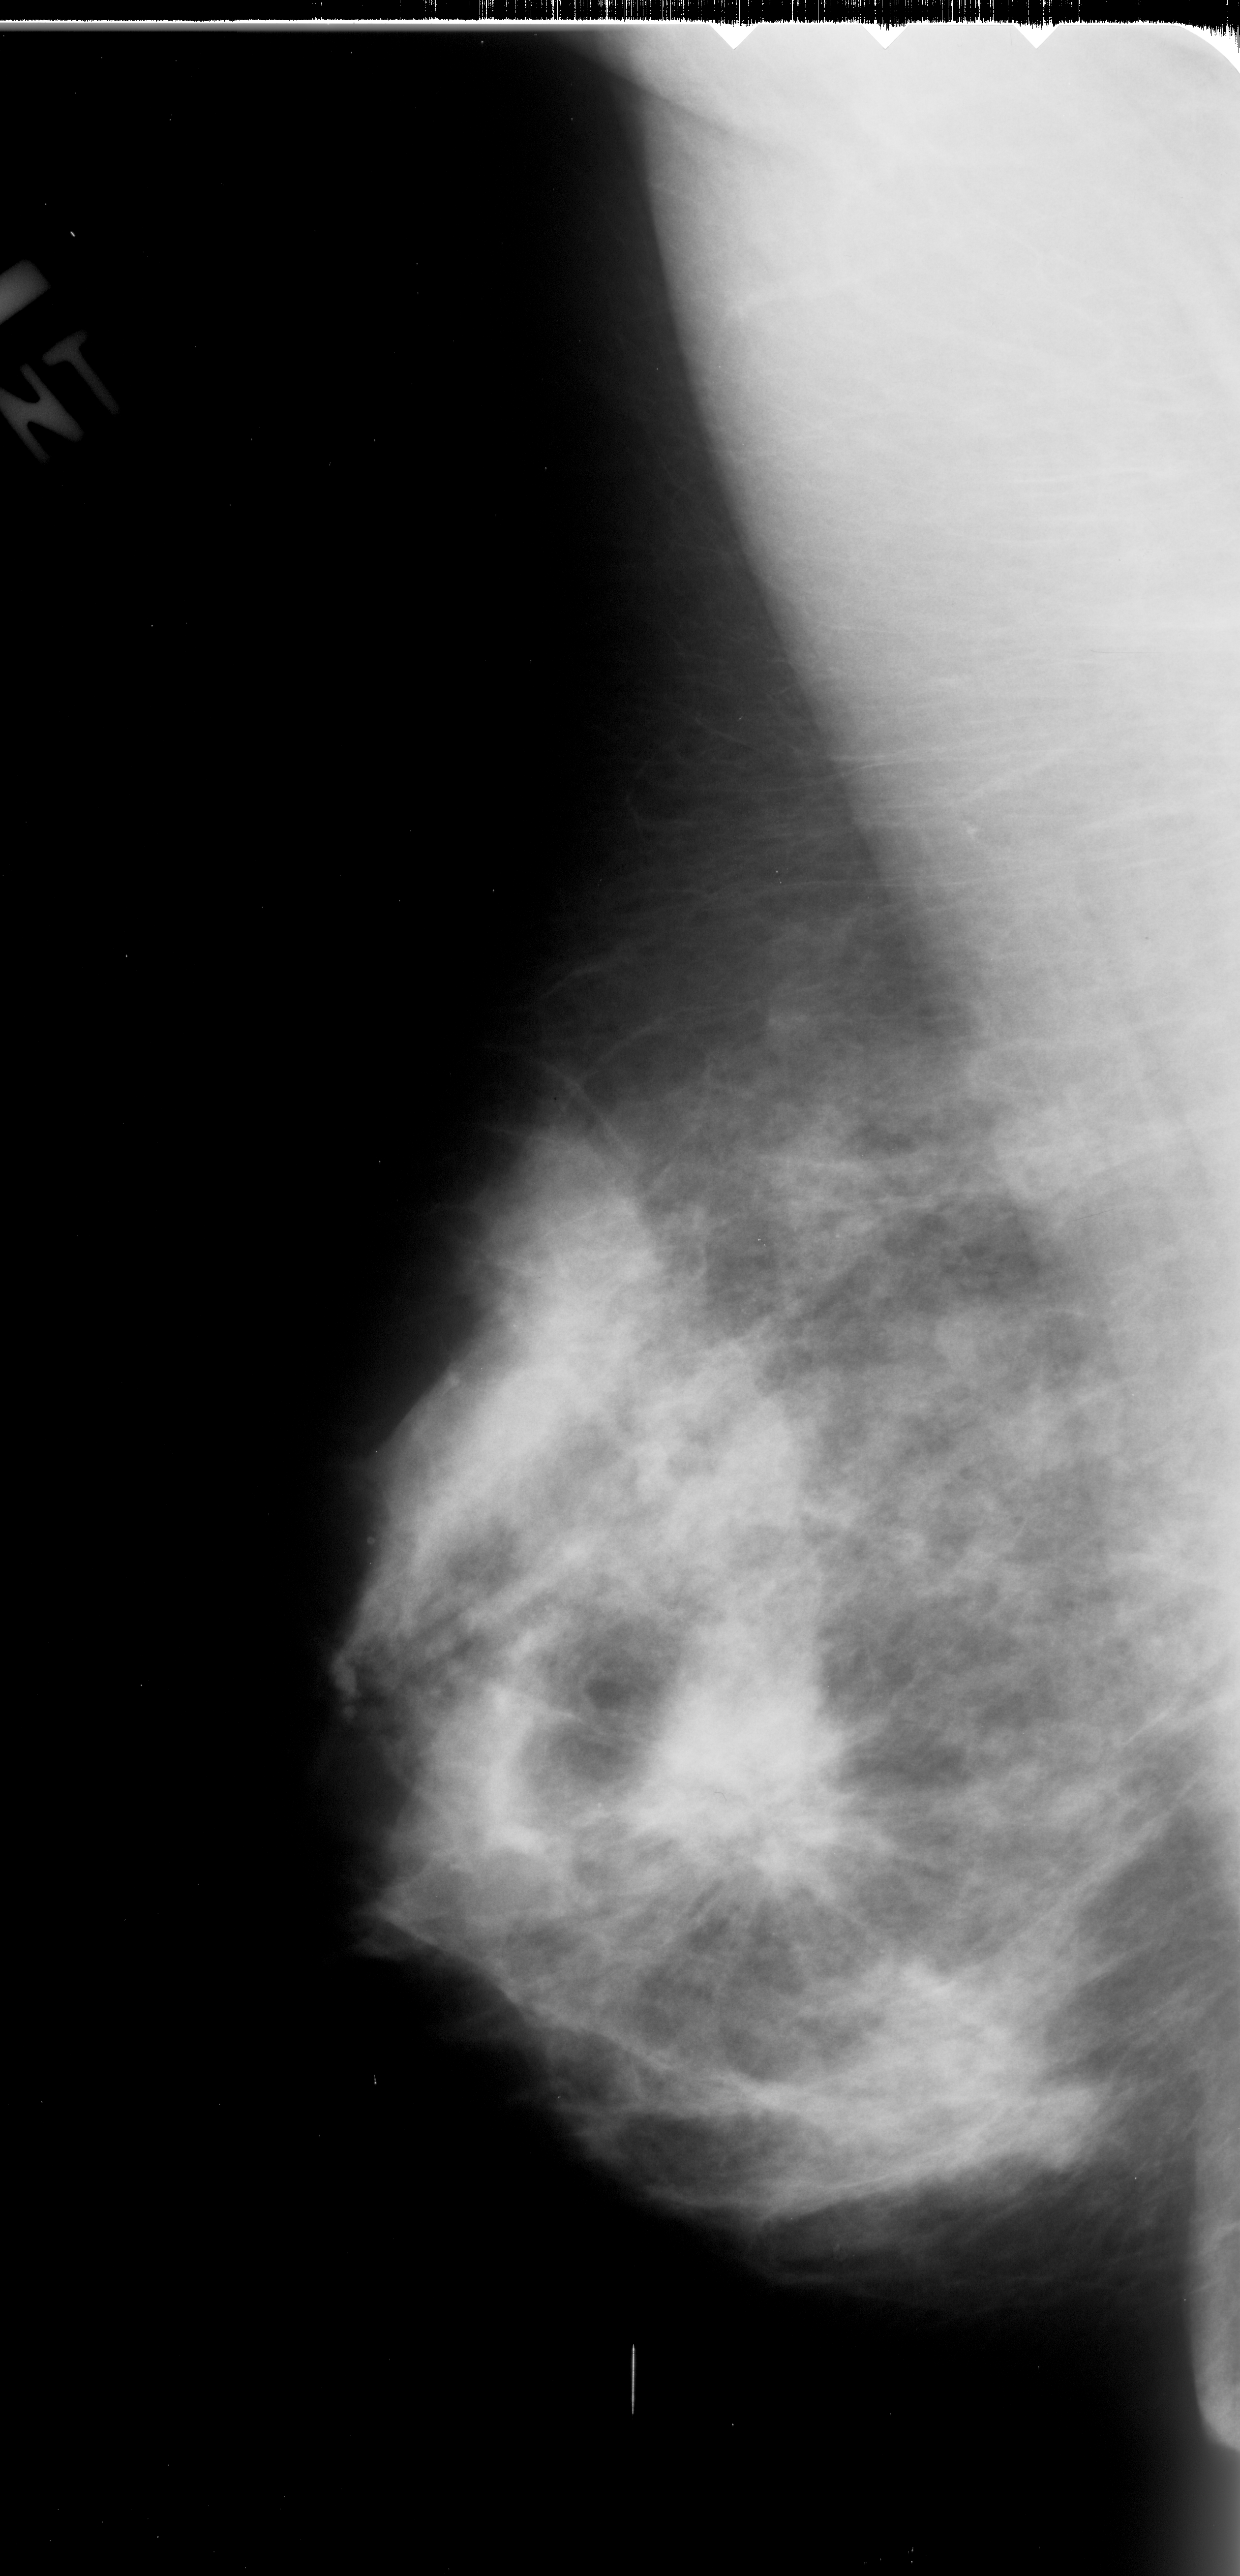
Digitized screen-film mammogram, left breast, mediolateral oblique (MLO) view.
Abnormality record for this image: mass, shape irregular, margins spiculated; BI-RADS assessment category 5; pathology result (as recorded, not read from the image): malignant.